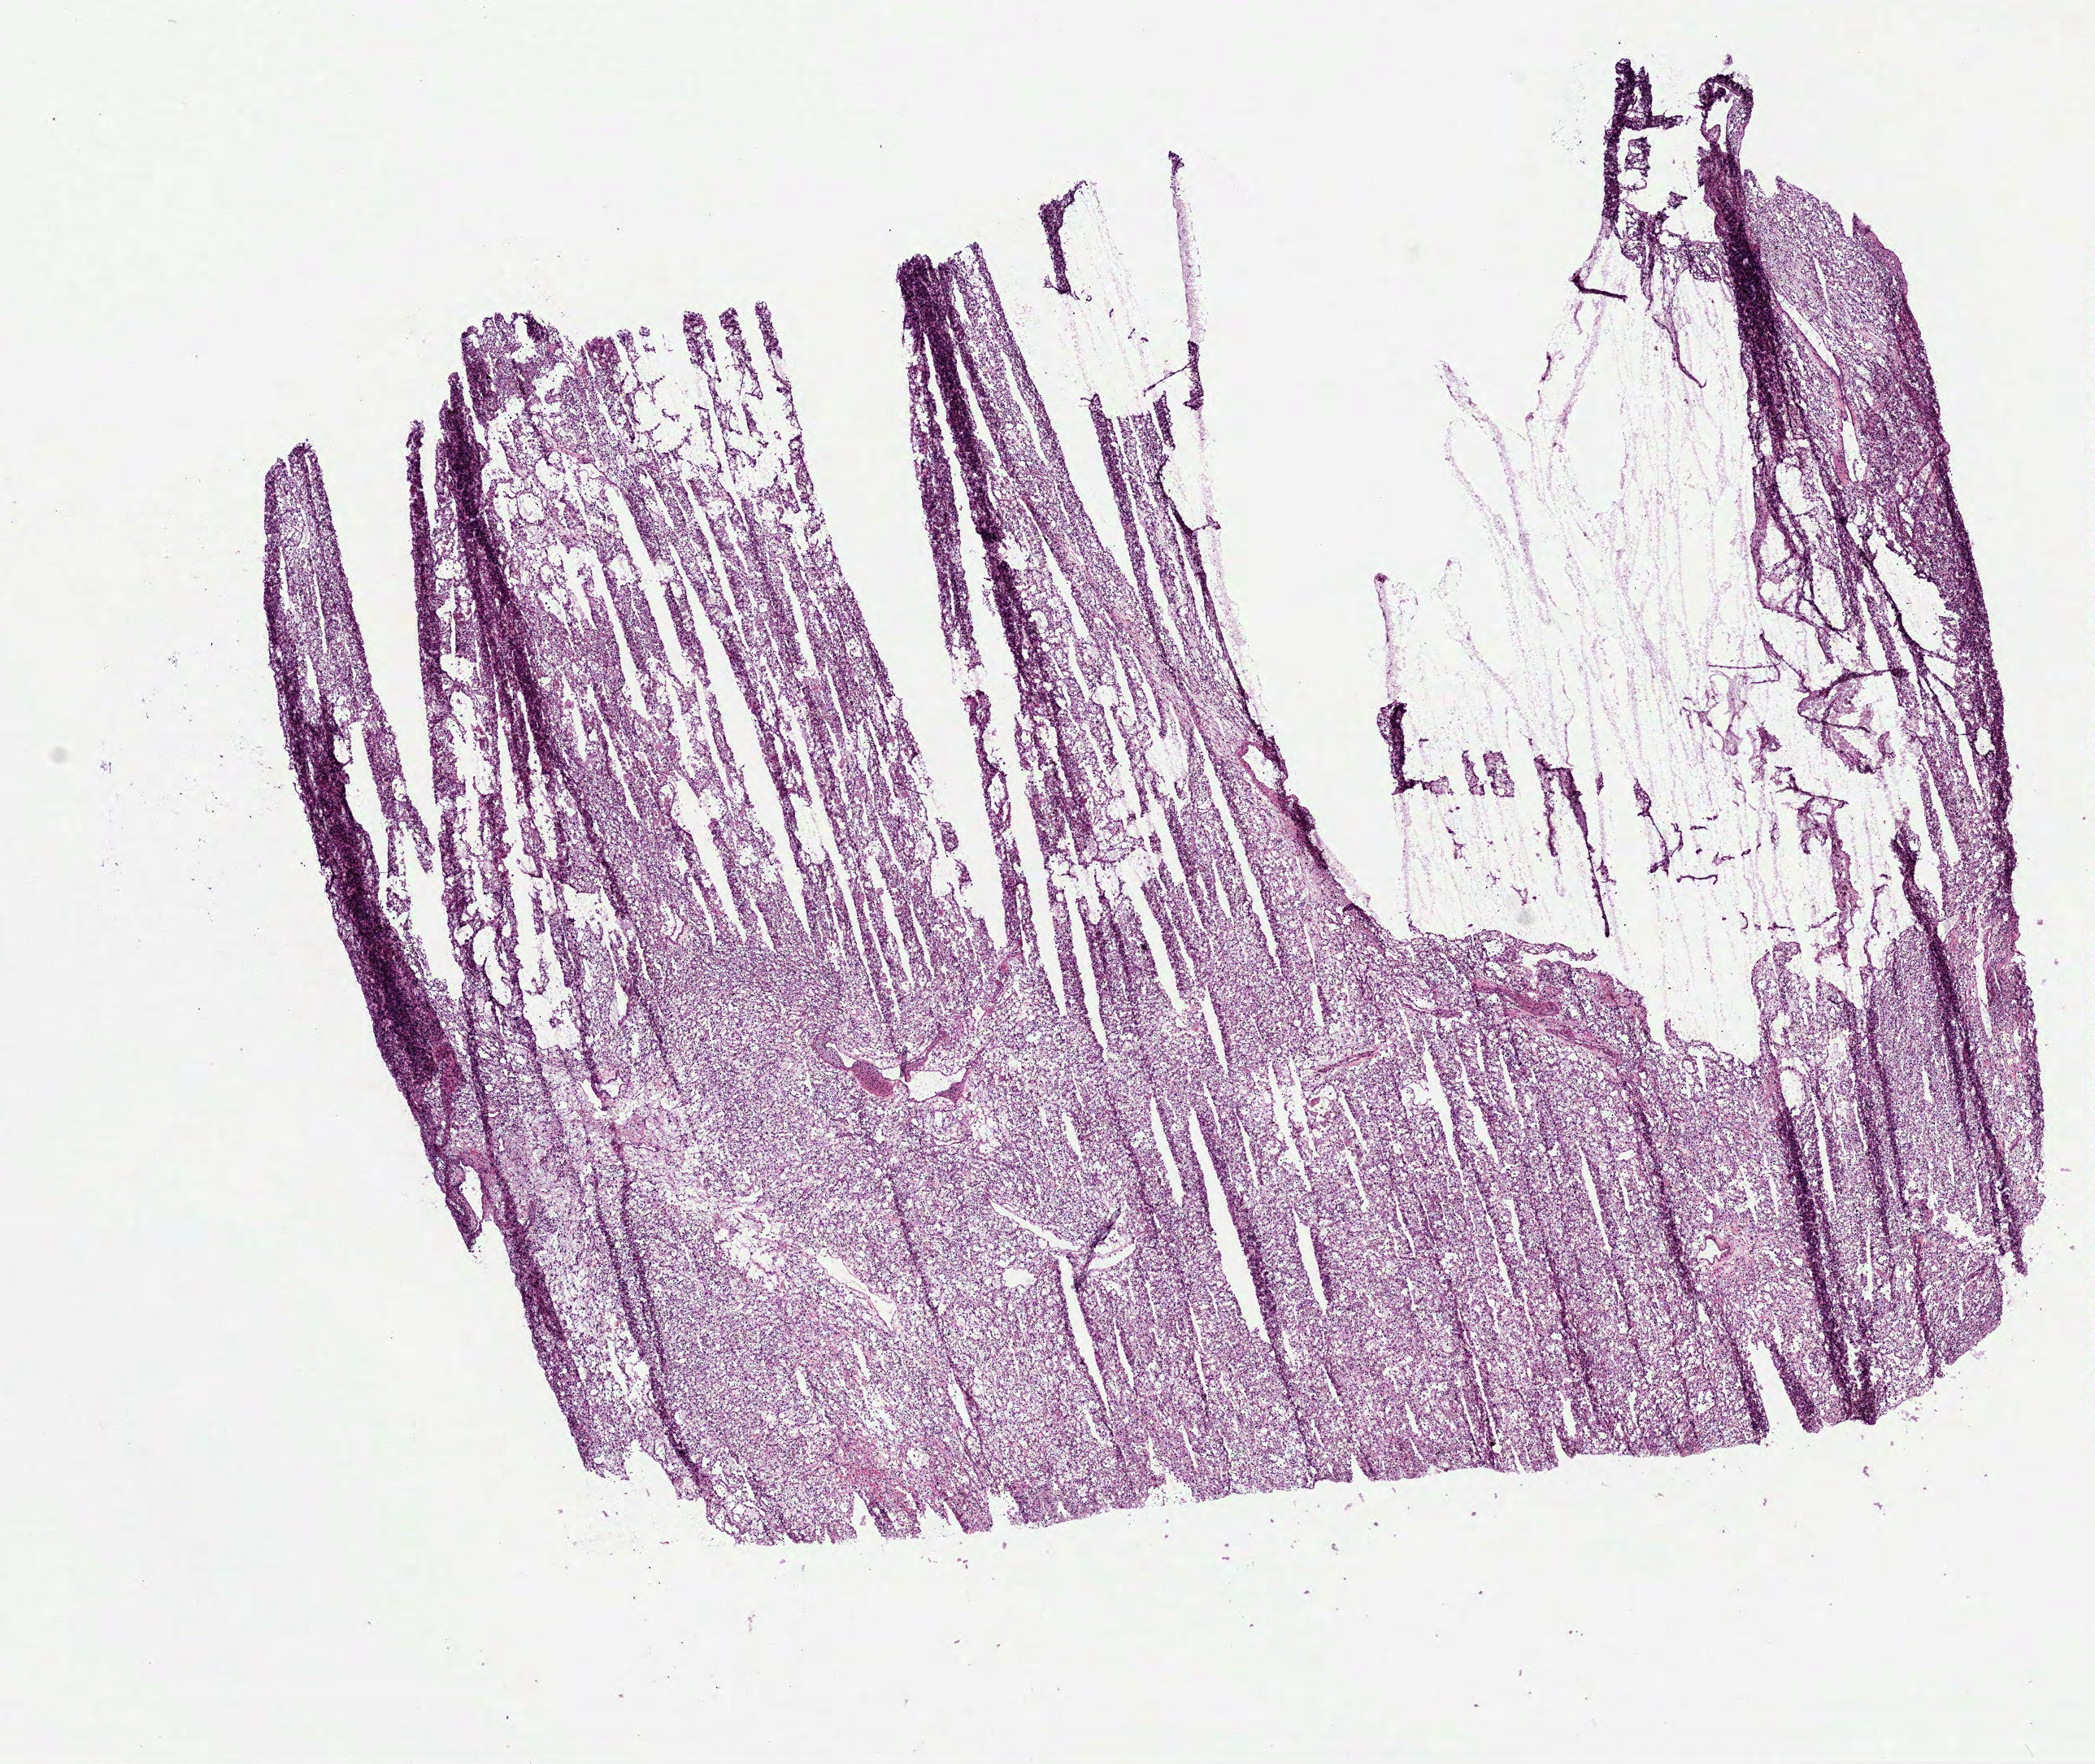
H&E-stained whole-slide image — whole scanned area (about 10.4 x 8.8 mm, from a 40x scan) shown as a low-resolution overview. Frozen section from the bottom of the tissue portion. Sample: primary tumour, kidney. Patient: male, age at initial diagnosis 55 years. Histologic grade: G2 (moderately differentiated). Pathologist review of this section (percent, as recorded): tumour cells 95%, tumour nuclei 85%, normal cells 0%, stromal cells 5%, necrosis 0%.
AJCC pathologic stage: I. Diagnosis: Clear cell adenocarcinoma, NOS.